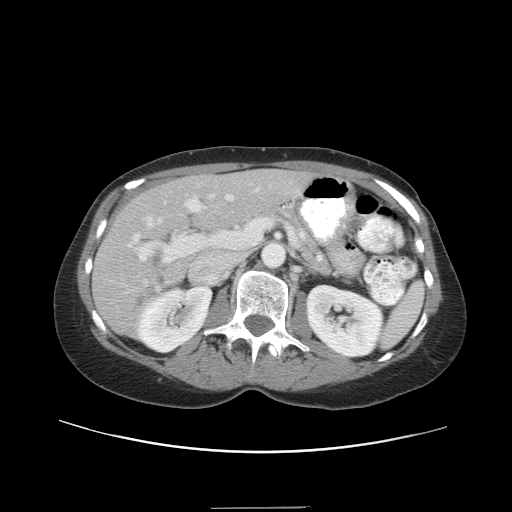
Contrast-enhanced abdominal CT, one axial slice; position 20 of 38 along the scan axis; reconstruction kernel STANDARD; soft-tissue window (W 400 / L 40 HU); 5 mm slice thickness; 512 × 512 image matrix, field of view 388 × 388 mm. Female patient, age 64 years. From the clinical record (not read from this slice): diagnosis: colorectal cancer liver metastases, imaged before liver resection; multiple liver metastases: no; largest metastasis: 3.8 cm; disease in both lobes: yes.
Annotated regions visible in this slice (outlined manually by an expert reader):
- hepatic veins: bounding box (x1, y1, x2, y2) in pixels: (144, 188, 259, 286)
- liver: (94, 168, 307, 334)
- planned liver remnant (the part of the liver to remain after resection): (139, 168, 307, 230)
- portal vein (with intrahepatic branches): (128, 194, 214, 262)
- liver metastasis: (152, 255, 161, 274)